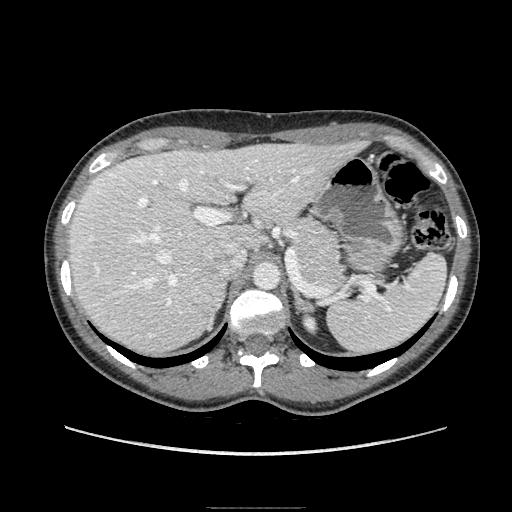
Contrast-enhanced abdominal CT, one axial slice; position 125 of 193 along the scan axis; soft-tissue window (W 400 / L 40 HU); 512 × 512 image matrix, field of view 380 × 380 mm. Female patient. Case-level facts recorded for this patient, not image findings: diagnosis: adrenocortical carcinoma; tumour side: right adrenal; tumour size at pathology: 3 cm; Ki-67 index: 4 %; stage (as recorded): 1.
Structures marked on this image (semi-automatically segmented with operator editing):
- mass: box from (x=195, y=271) to (x=229, y=323) px